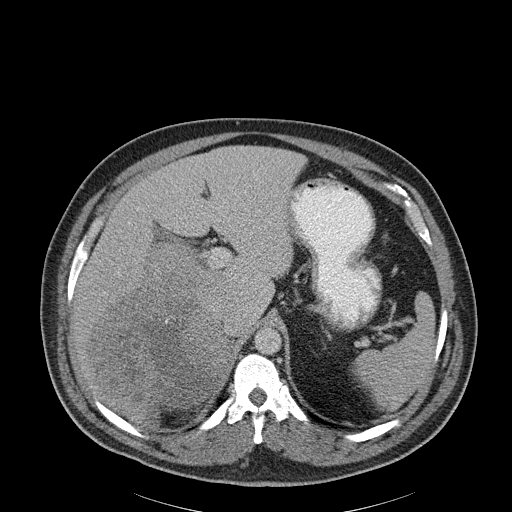
Contrast-enhanced abdominal CT, one axial slice. Slice 143 of 186 in the series (ordered by position). Reconstruction kernel B30f. 120 kVp. Soft-tissue window (W 400 / L 40 HU). 3 mm slice thickness. 512 × 512 image matrix. Patient: male, 56 years. Case-level facts recorded for this patient, not image findings: diagnosis: adrenocortical carcinoma; tumour side: right adrenal; tumour size at pathology: 18 cm; Ki-67 index: 2 %; stage (as recorded): 3.
Annotated regions visible in this slice (semi-automatically segmented with operator editing):
- mass: bounding box [x1, y1, x2, y2] px = [92, 243, 225, 419]